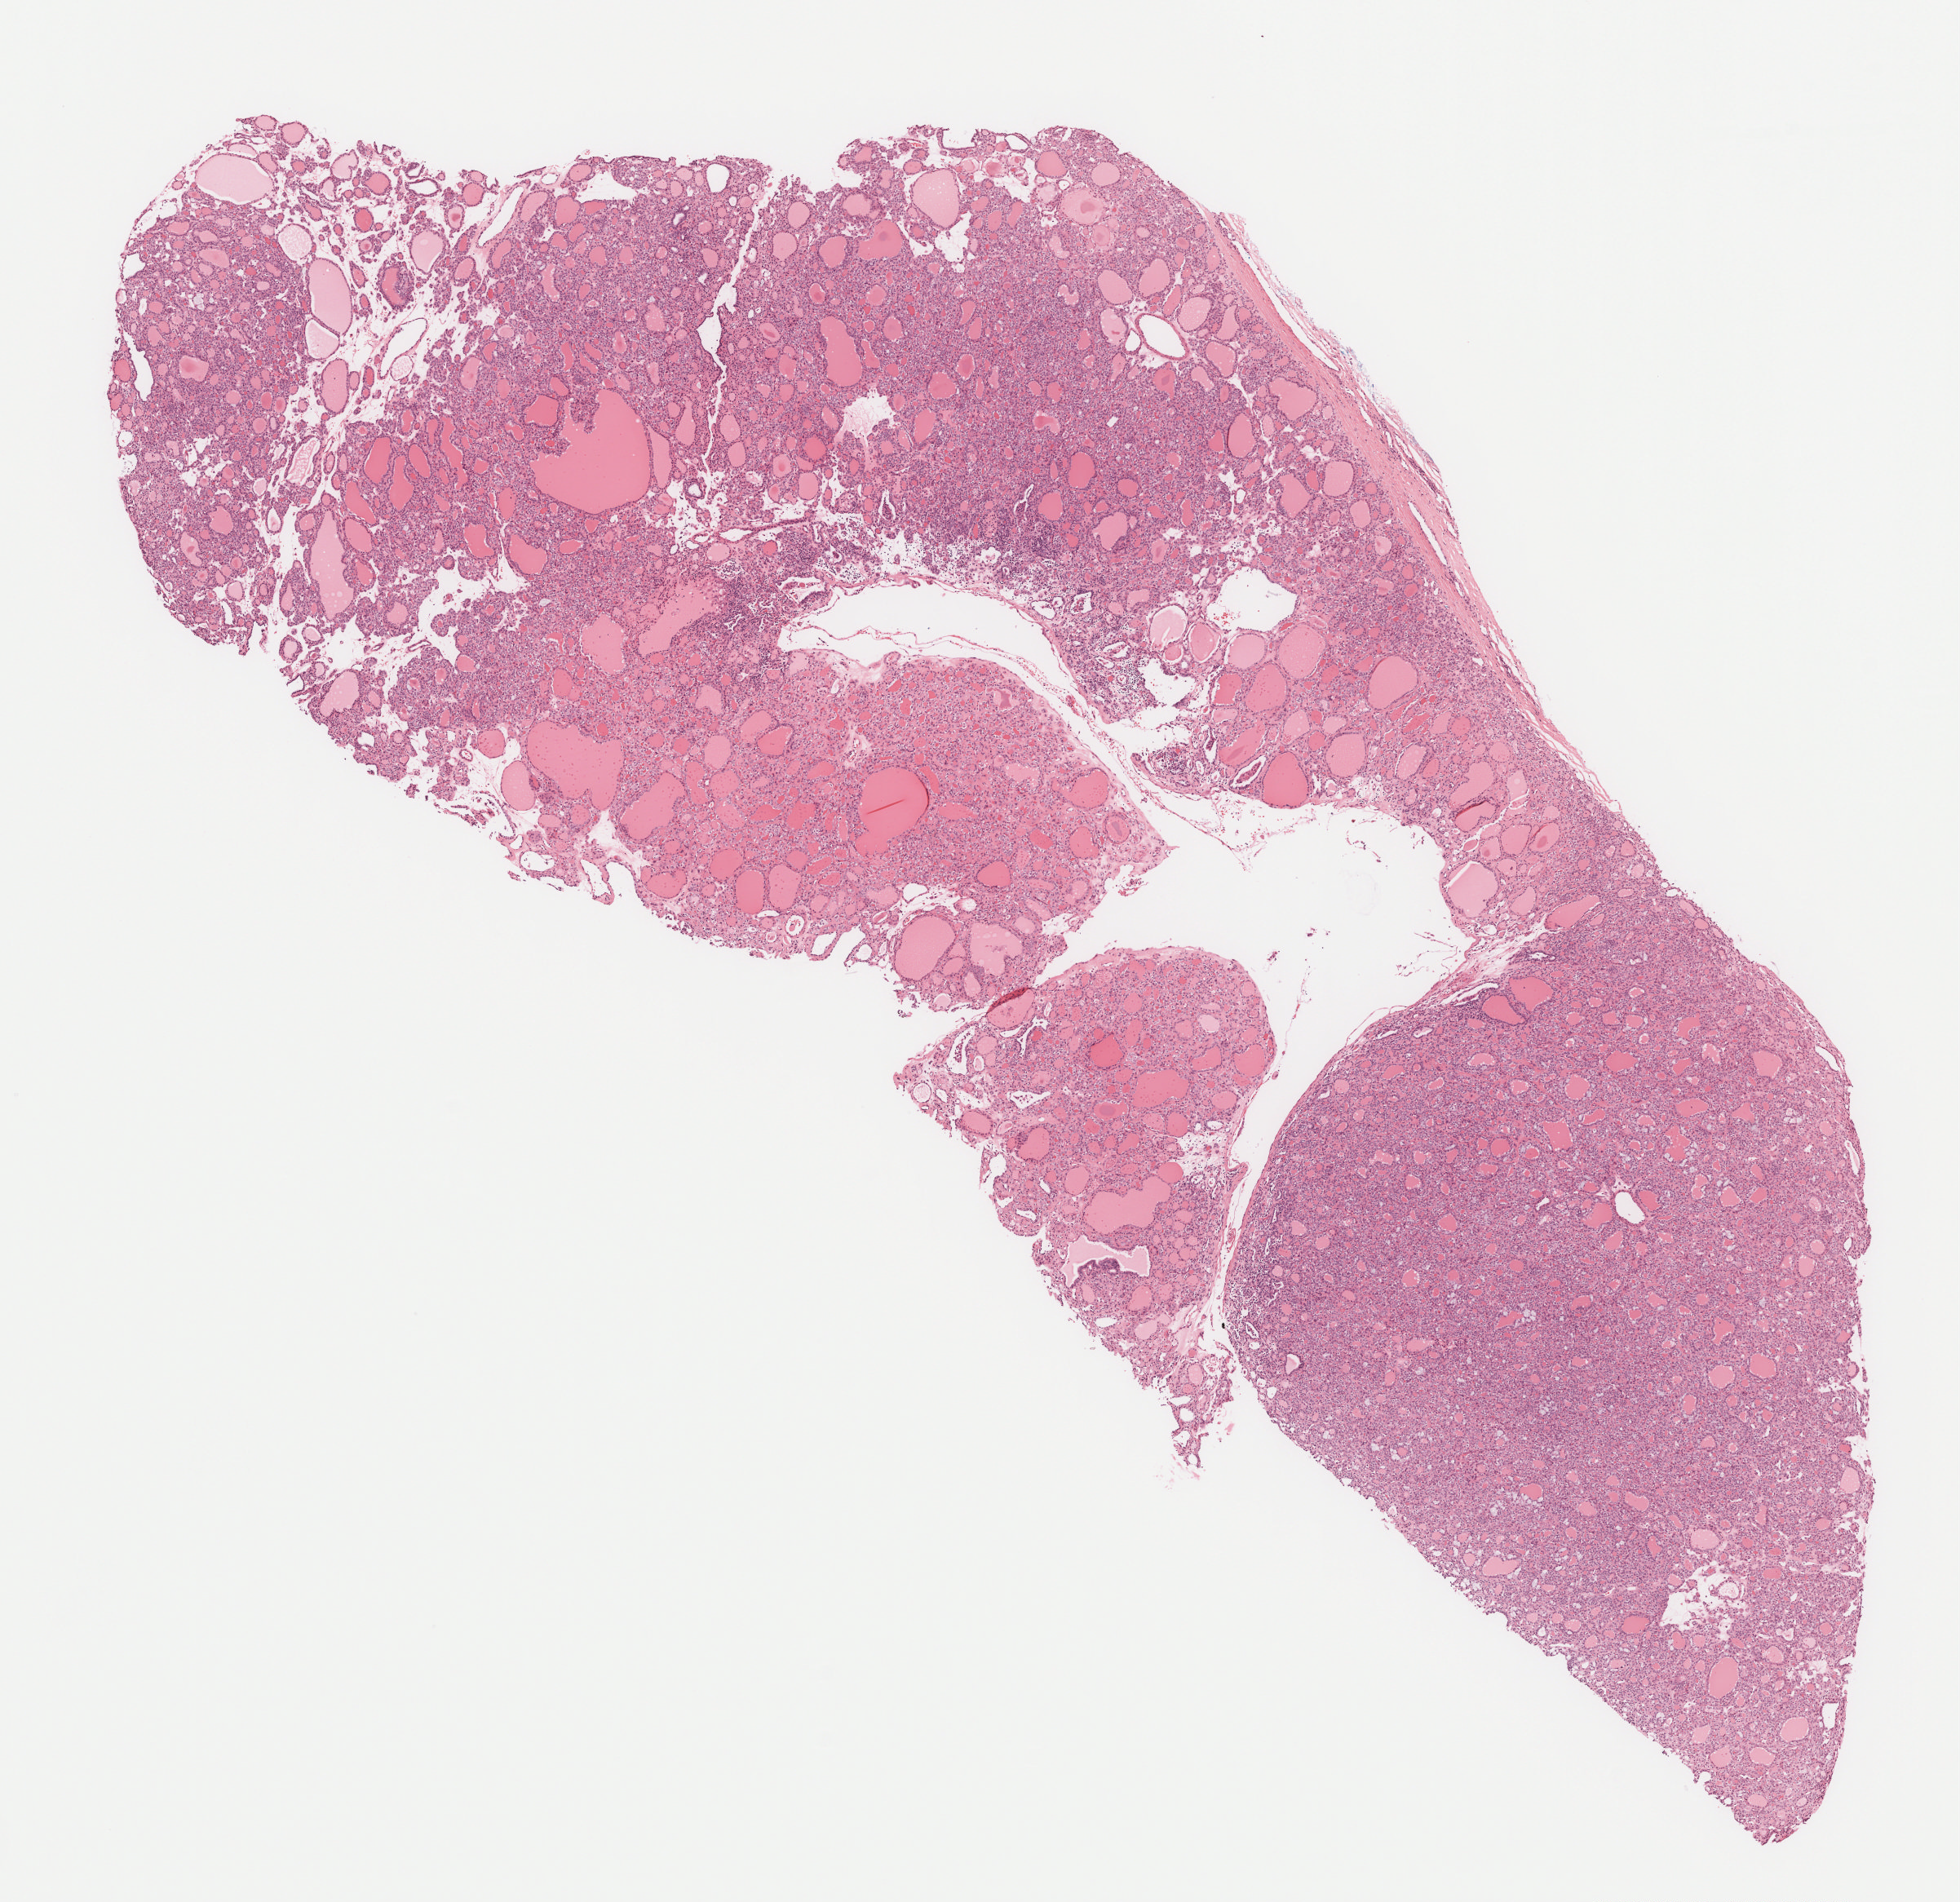
H&E-stained whole-slide image — low-resolution overview of the scanned area, about 9.7 x 9.4 mm (acquisition: 40x scan); formalin-fixed paraffin-embedded (FFPE) diagnostic section; thyroid, primary tumour sample. Patient: female, age at initial diagnosis 45 years.
• AJCC pathologic stage: I
• lymph nodes positive (case pathology): 0 of 14 examined
• histologic diagnosis: Papillary carcinoma, follicular variant (thyroid gland)
• laterality: right